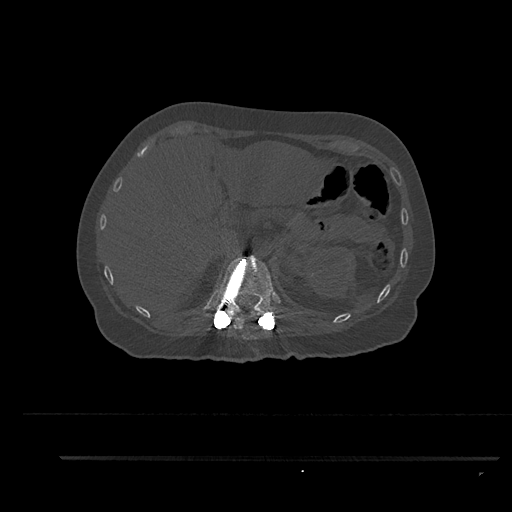
CT including the spine, one axial slice; slice 279 of 797 in the series (ordered by position); bone window (W 1800 / L 400 HU); 0.5 mm slice thickness; 512 × 512 image matrix, field of view 408 × 408 mm. Female patient, age 44 years. Case-level facts recorded for this patient, not image findings: primary cancer: renal; vertebrae with lytic lesions (as recorded): L1.
Annotated regions visible in this slice (semi-automatic segmentation, software-assisted and operator-edited):
- T11 vertebra: bounding box (x1, y1, x2, y2) in pixels: (233, 313, 255, 340)
- T12 vertebra: (214, 251, 282, 327)